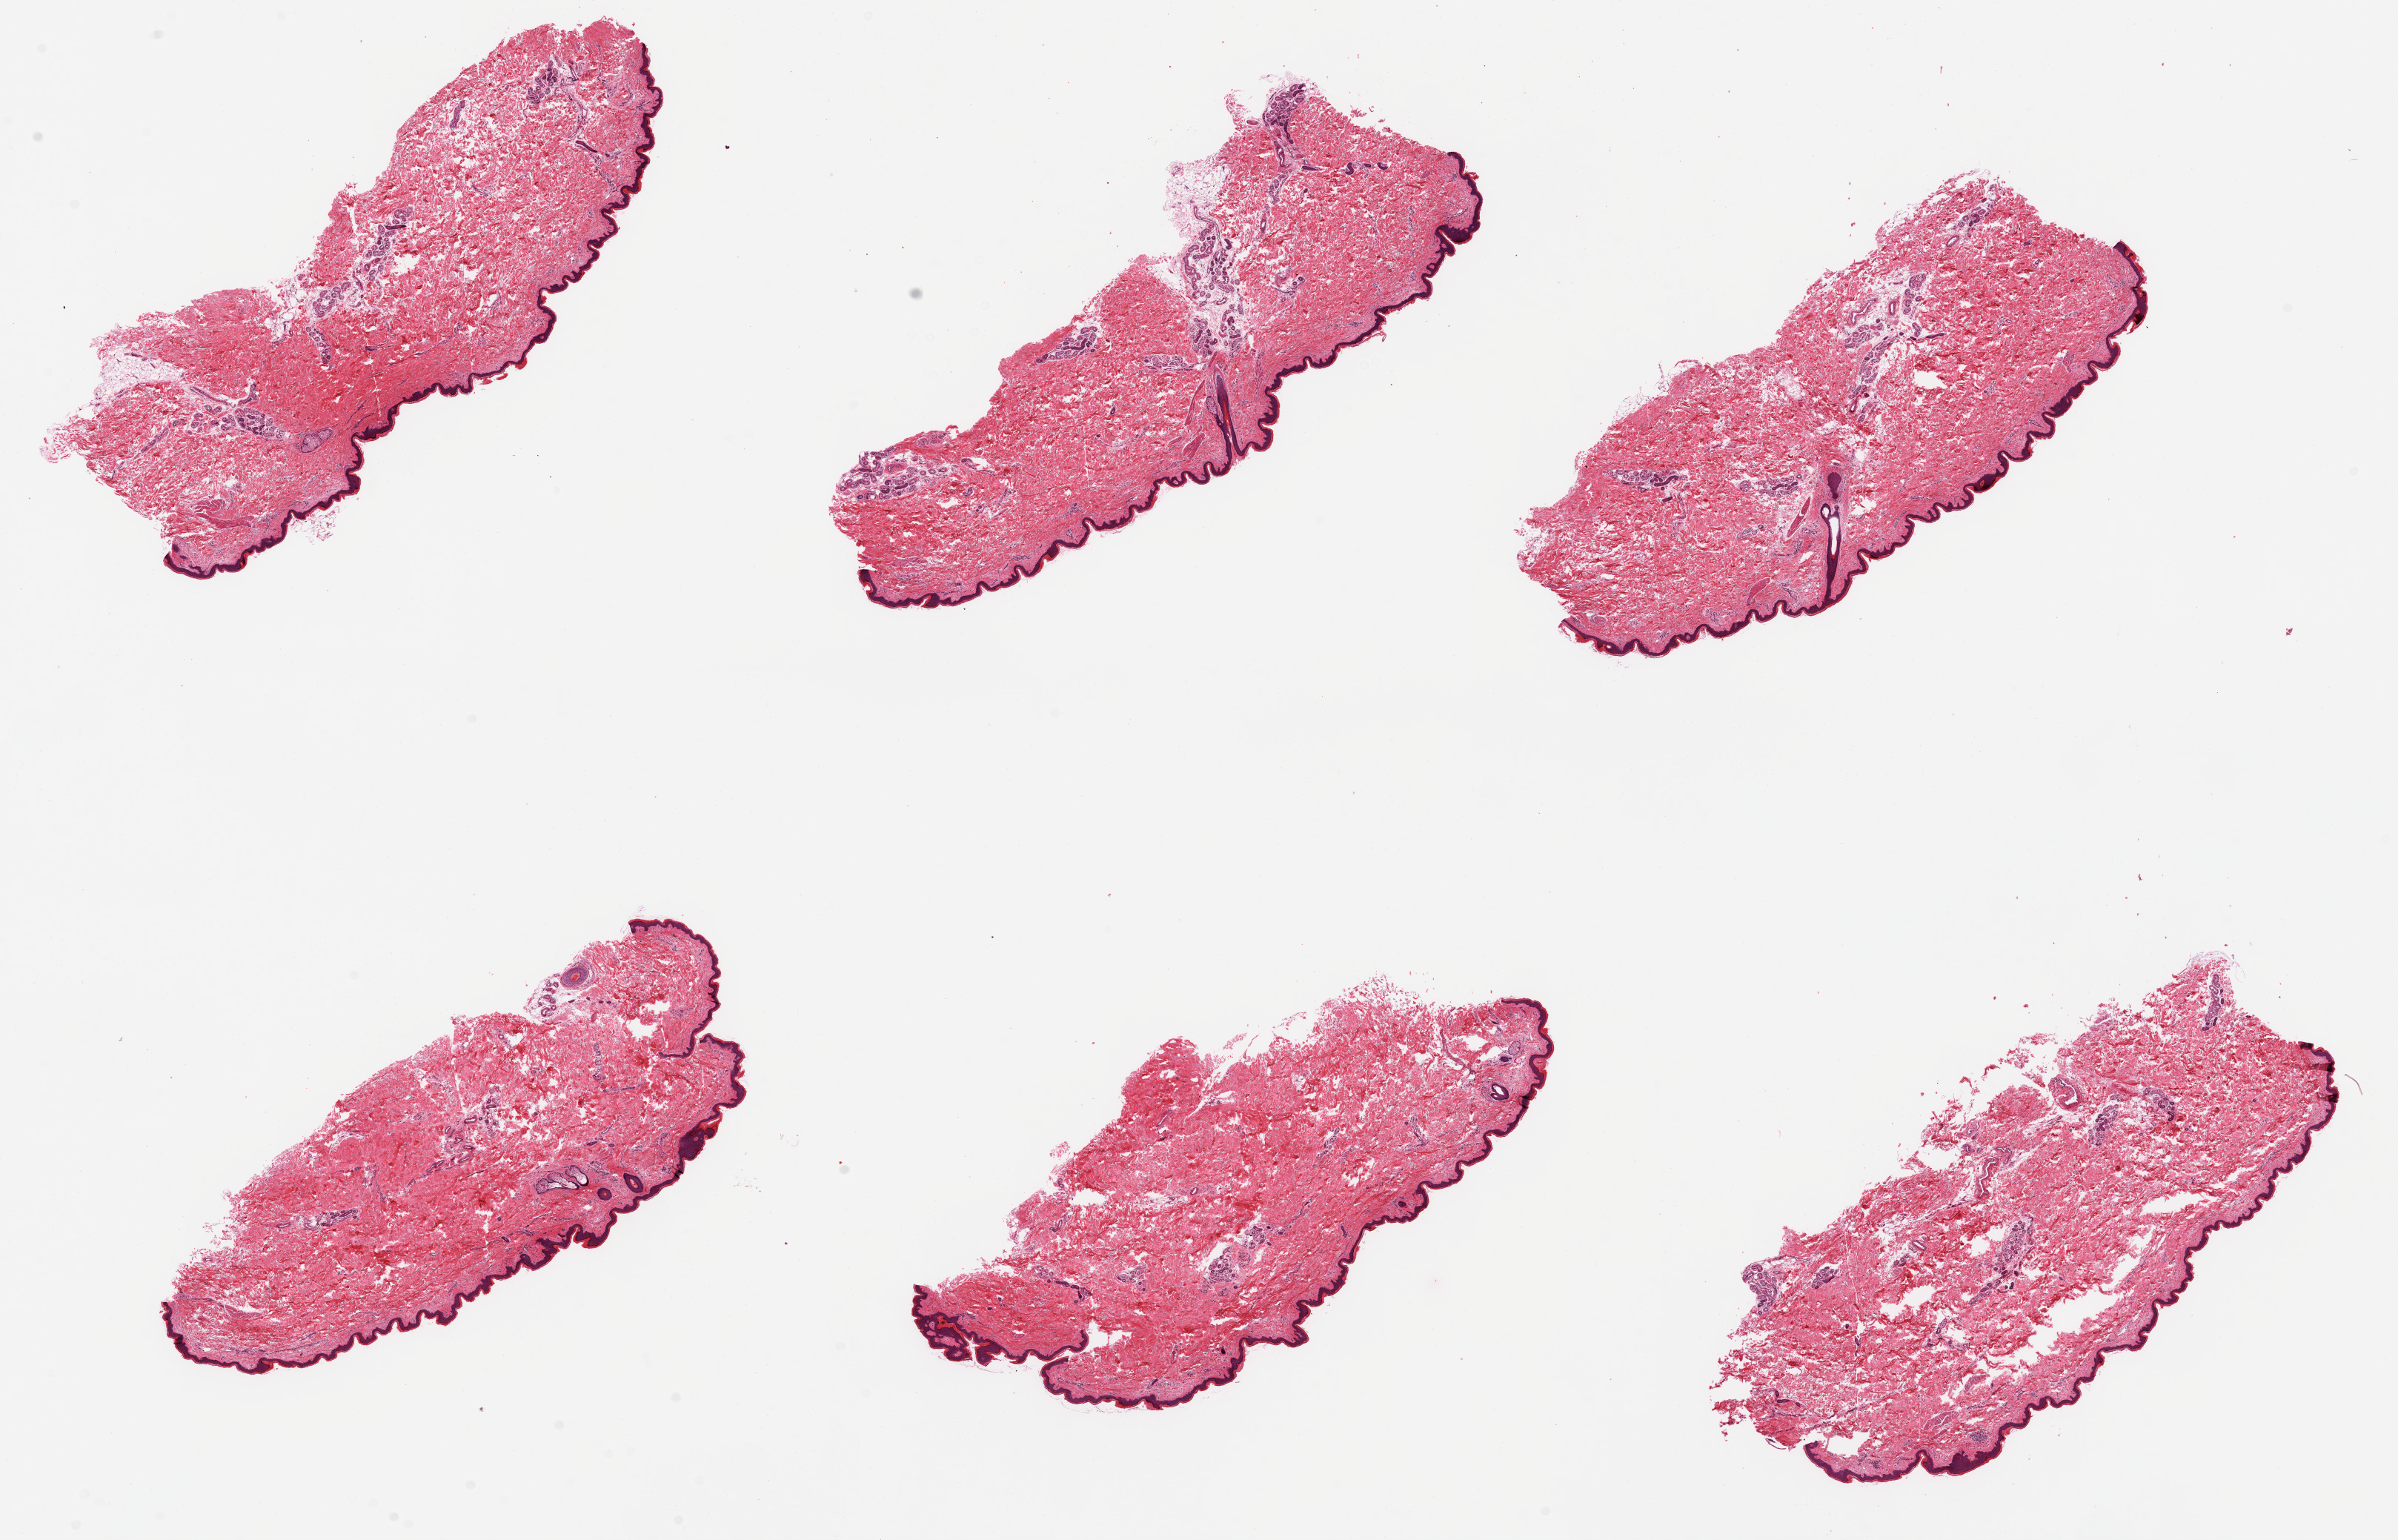
H&E whole-slide image, brightfield — whole scanned area (about 25.6 x 16.4 mm) shown as a low-resolution overview. PAXgene-fixed, paraffin-embedded tissue. Target tissue: skin of lower leg. Tissue donor sample.
• reviewer comment on this tissue sample: 6 pieces, minimal dermal fat;squamous epithelium is ~50-6-microns